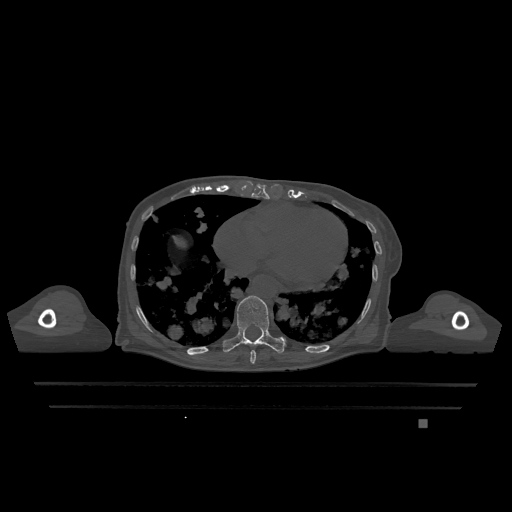
CT including the spine, one axial slice; position 652 of 1317 along the scan axis; bone window (W 1800 / L 400 HU); 0.5 mm slice thickness; 512 × 512 image matrix, field of view 500 × 500 mm. Female patient, age 74 years. From the clinical record (not read from this slice): primary cancer: lung; vertebrae with lytic lesions (as recorded): T1, T4, T5, T6, L4, L5.
Outlined on this slice (semi-automatically segmented with operator editing):
- T10 vertebra: bounding box (x1, y1, x2, y2) in pixels: (222, 295, 286, 353)
- T9 vertebra: (250, 350, 256, 364)